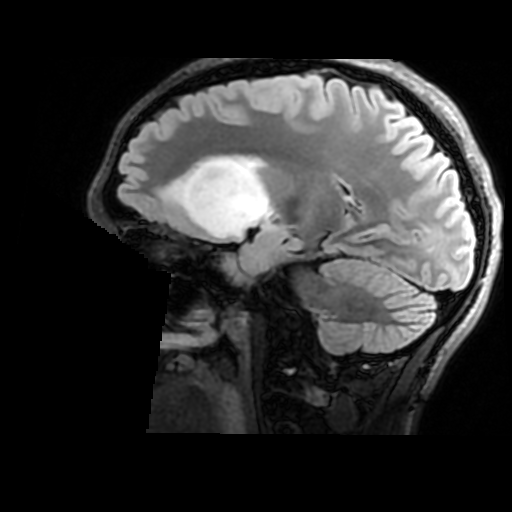
Brain MRI from a brain-tumour surgery series, one sagittal slice; position 105 of 176 along the scan axis; T2 FLAIR; 1 mm slice thickness; 512 × 512 image matrix, field of view 240 × 240 mm. Case-level facts recorded for this patient, not image findings: histopathology: Astrocytoma; WHO grade: 2; IDH mutation: yes; tumour location: Right Insular.
Structures marked on this image (manually delineated by an expert):
- tumour: bounding box [x1, y1, x2, y2] px = [167, 155, 277, 238]